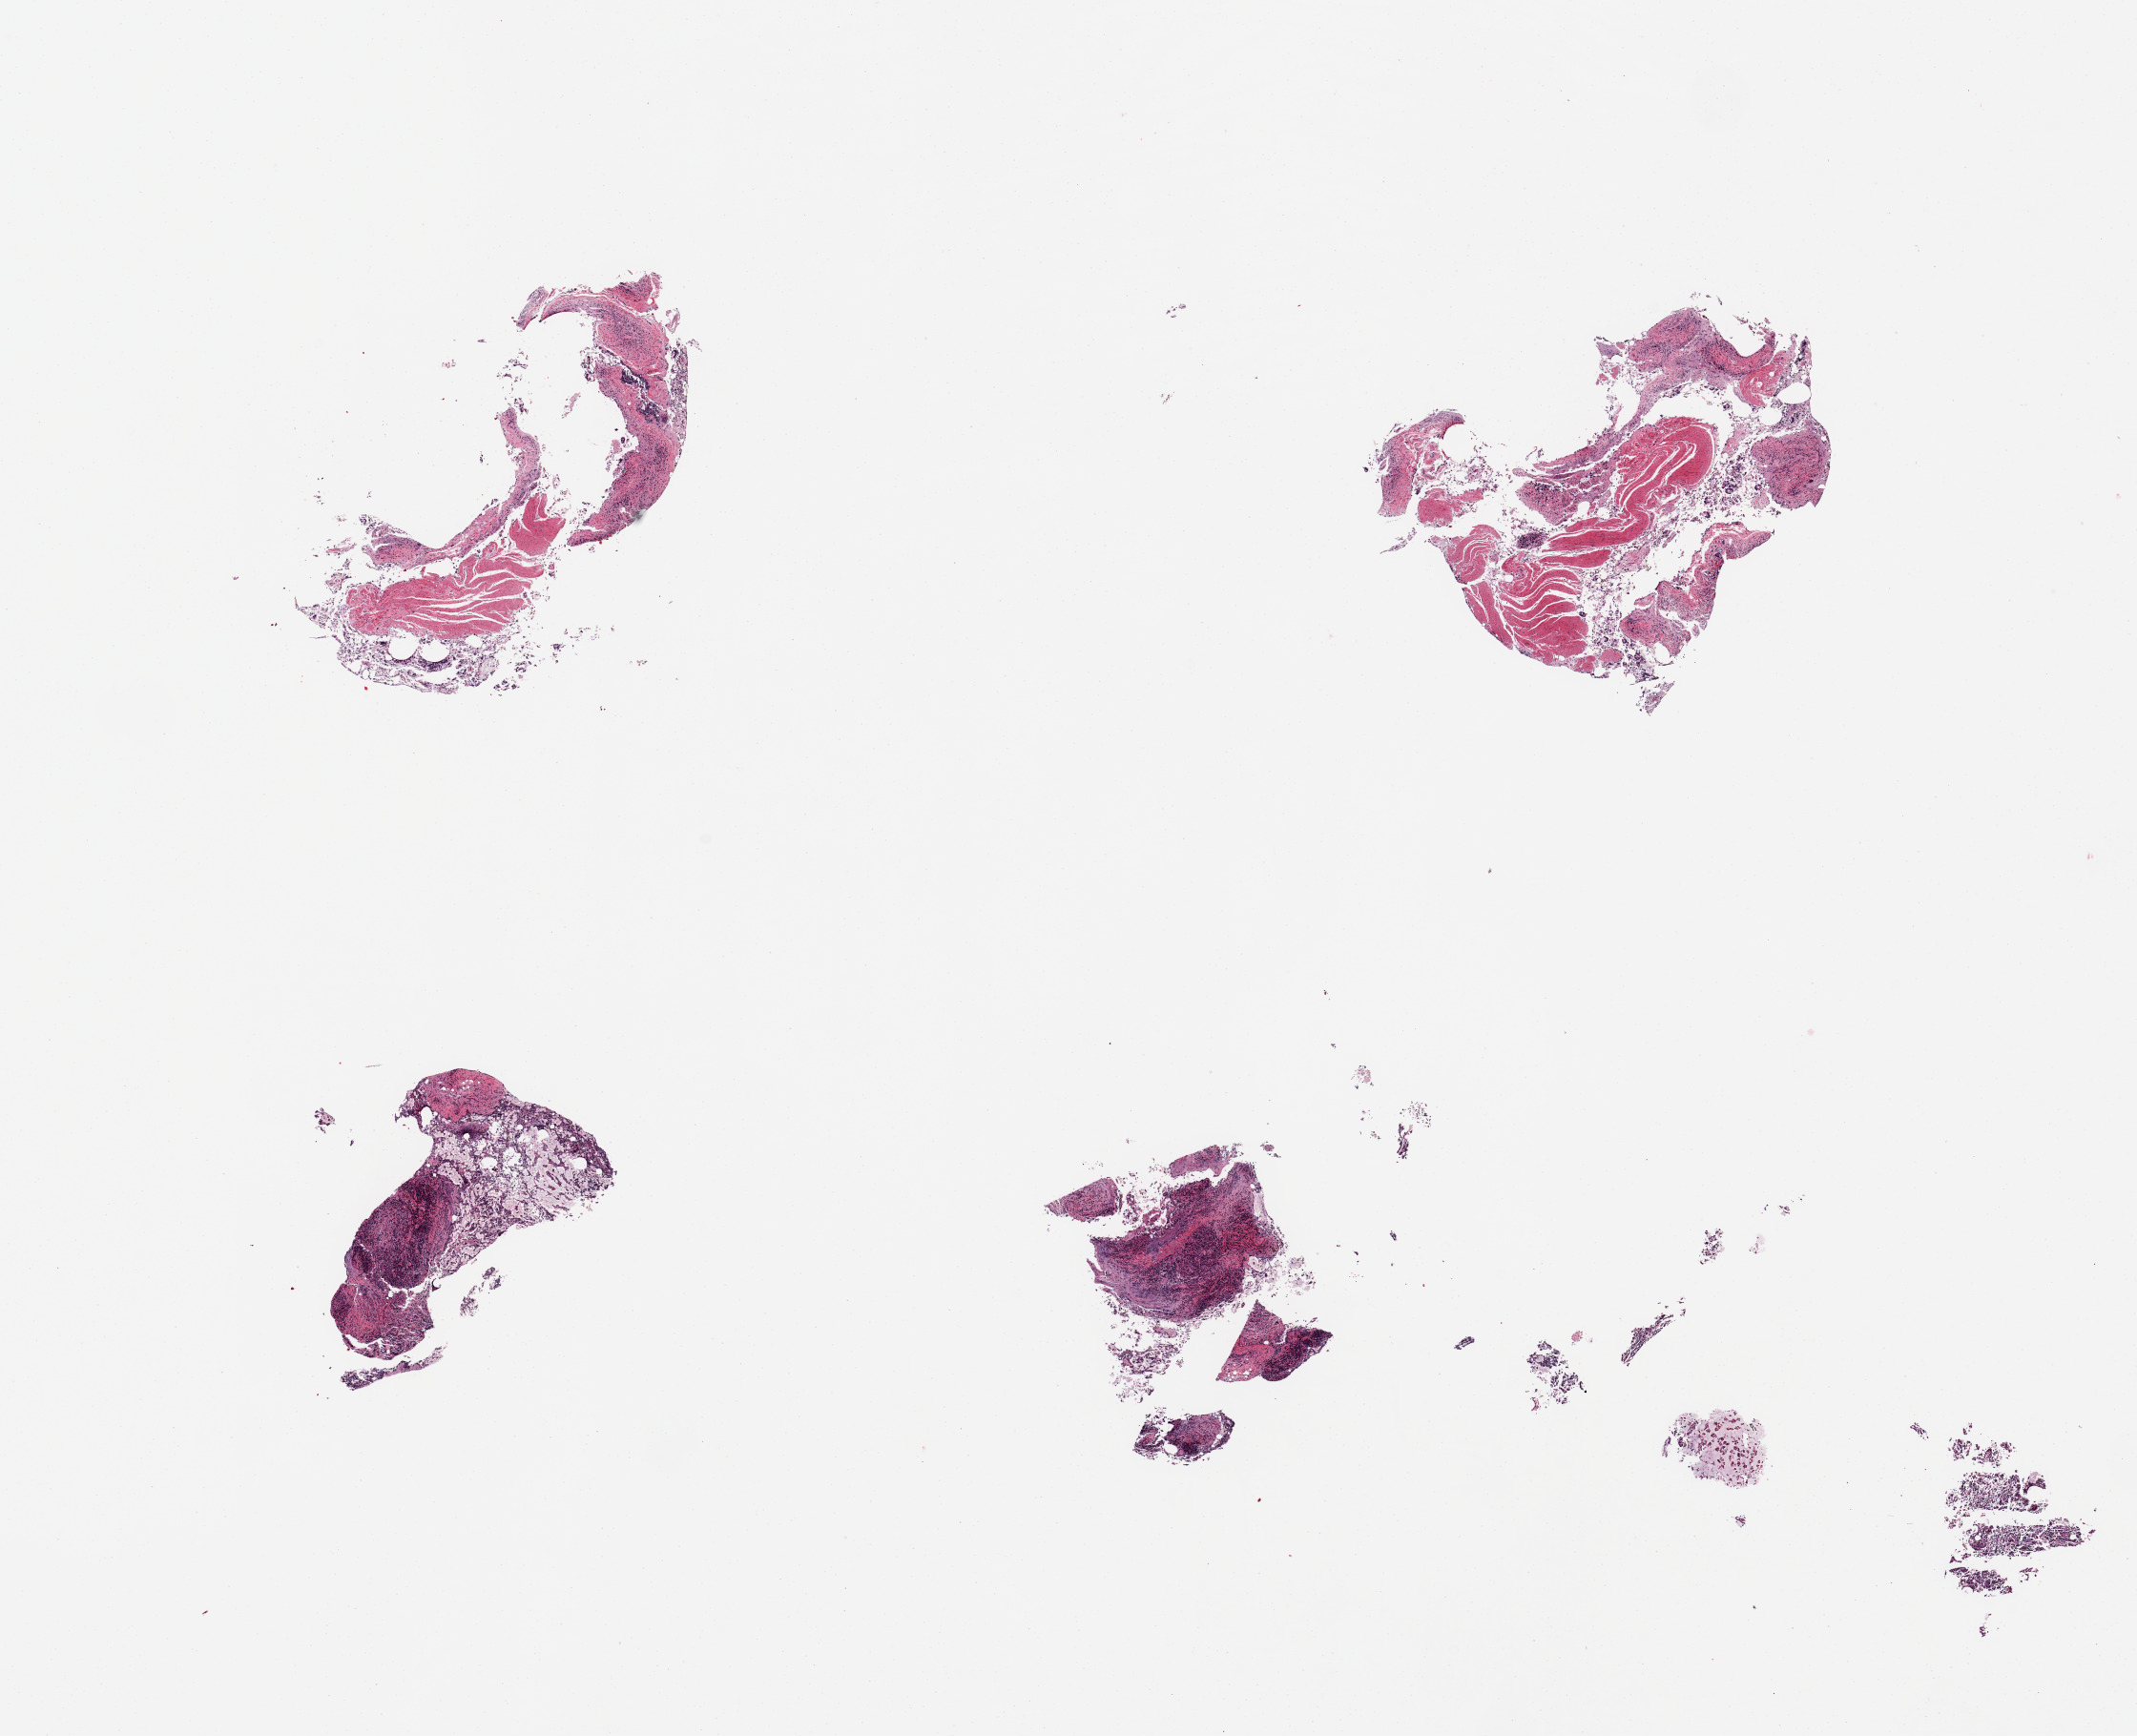
Whole-slide image, H&E stain, brightfield — shown as a low-resolution overview of the whole scanned area (about 17.7 x 14.4 mm, from a 20x scan). Donor sex: female.
* specimen: PAXgene-fixed, paraffin-embedded tissue; section of ileum (target tissue); tissue donor sample